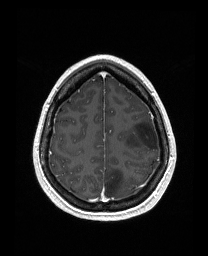
Brain MRI from a brain-tumour surgery series, one axial slice; position 126 of 176 along the scan axis; T1-weighted post-contrast; 1 mm slice thickness; 208 × 256 image matrix, field of view 203 × 250 mm. From the clinical record (not read from this slice): histopathology: Astrocytoma; WHO grade: 3; IDH mutation: yes; tumour location: Left Frontal.
Outlined on this slice (outlined manually by an expert reader):
- tumour: bounding box (x1, y1, x2, y2) in pixels: (125, 118, 159, 151)